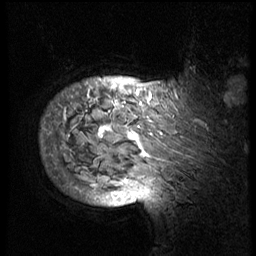
Breast MRI (dynamic contrast-enhanced), one sagittal slice; slice 63 of 74 in the series (ordered by position); 3 images stored at this slice position (order not interpretable as contrast timing); 1.5 T; TE 4.2 ms, TR 8.9 ms; 2.5 mm slice thickness; 256 × 256 image matrix, field of view 200 × 200 mm. Female patient, age 57 years. From the clinical record (not read from this slice): setting: breast cancer imaged before/during neoadjuvant chemotherapy; receptor status: HER2-positive.
Structures marked on this image (semi-automatic segmentation, software-assisted and operator-edited):
- analysis volume of interest (the breast-tissue region the enhancement analysis was run in; not a lesion): bounding box [x1, y1, x2, y2] px = [40, 62, 239, 175]
- tumour enhancement mask (voxels above the 140 % enhancement threshold inside the analysis volume of interest): [56, 86, 202, 158]